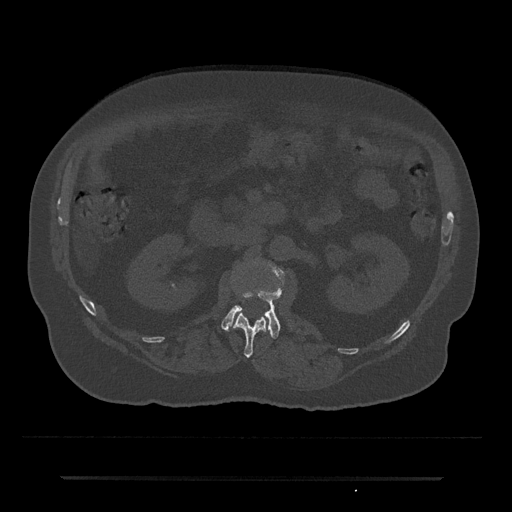
CT including the spine, one axial slice; position 38 of 797 along the scan axis; 120 kVp; bone window (W 1800 / L 400 HU); 0.5 mm slice thickness; 512 × 512 image matrix. Male patient, age 69 years. Case-level facts recorded for this patient, not image findings: primary cancer: prostate.
Outlined on this slice (semi-automatic segmentation, software-assisted and operator-edited):
- L1 vertebra: bounding box [x1, y1, x2, y2] px = [233, 313, 267, 358]
- L2 vertebra: [221, 266, 285, 339]